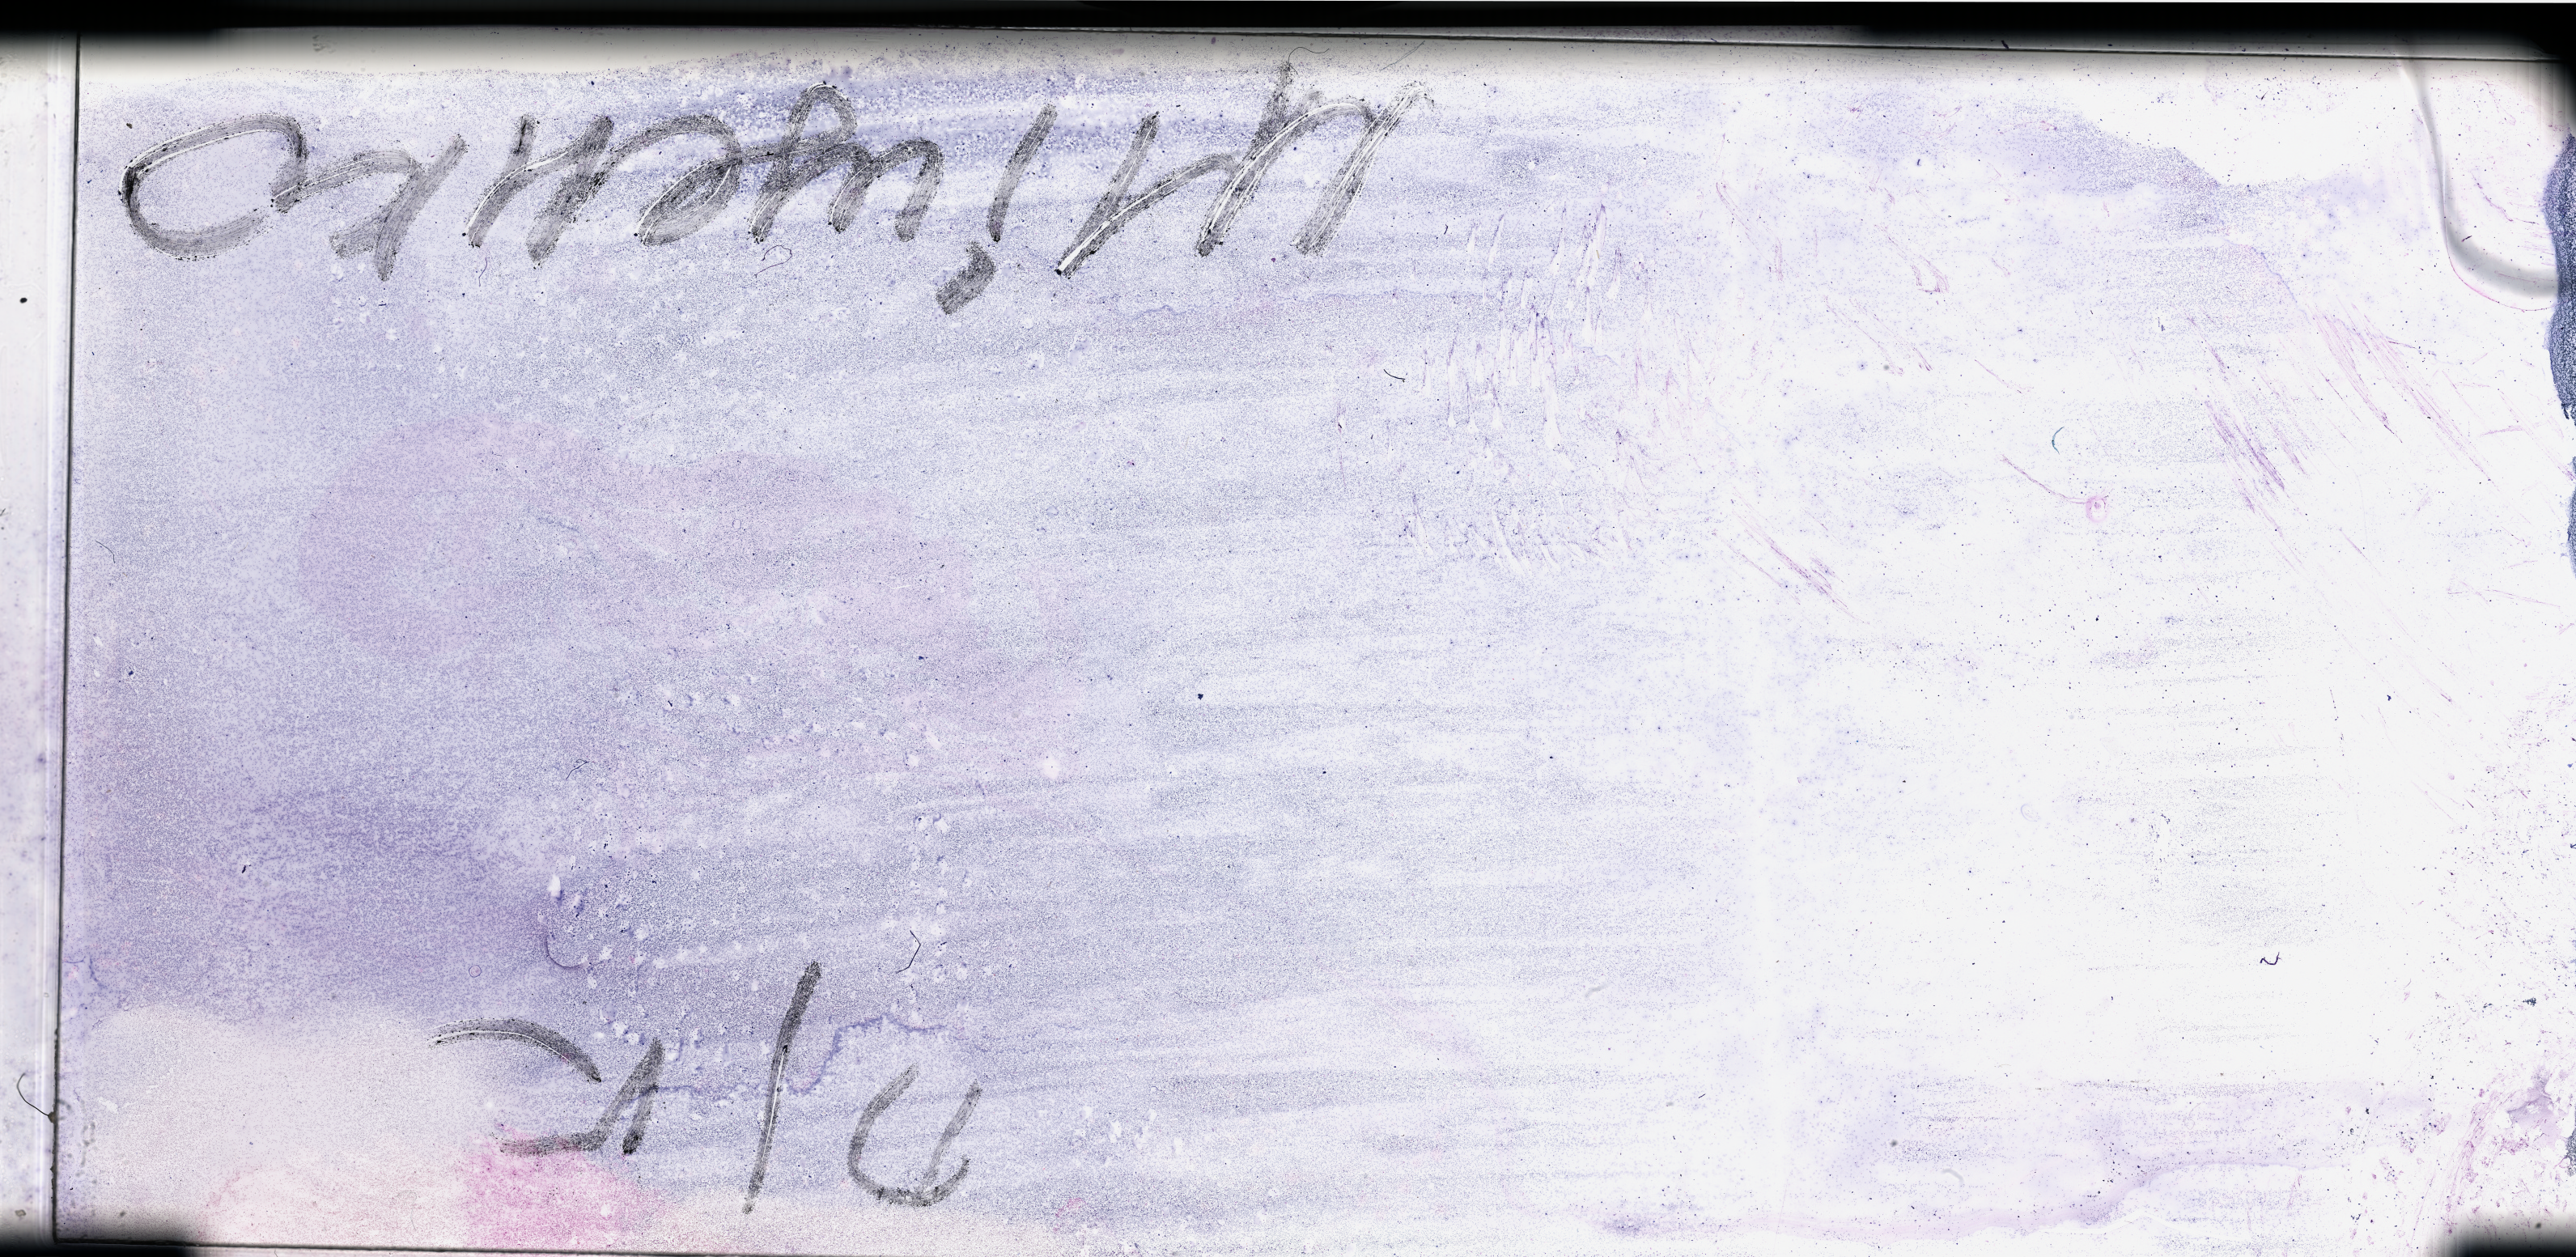
Hematoxylin and eosin (H&E) stained whole-slide image — shown as a low-resolution overview of the whole scanned area (about 50.3 x 24.5 mm, slide scanned at 40x). Peripheral blood (leukaemic) sample. Patient: male, age 45 years.
Diagnosis: Acute Myeloid Leukemia.